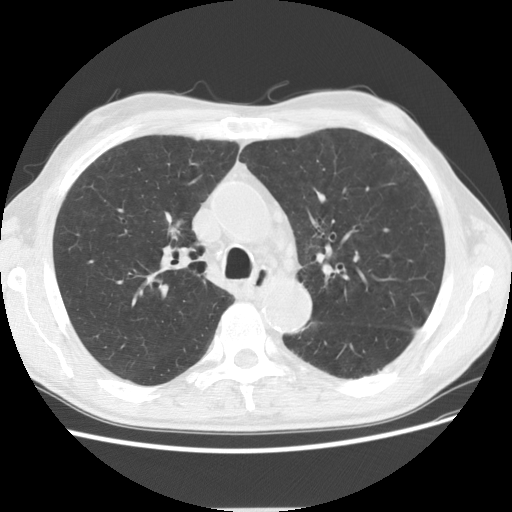
Chest CT (low-dose screening protocol), one axial image. Baseline annual screen. Lung window (W 1500 / L -600 HU). 2.5 mm slice thickness. Standard (soft-tissue) reconstruction kernel (STANDARD). 120 kVp. 512 × 512 image matrix. Male participant, aged 73 years at enrolment. Current smoker at enrolment.
• Expert reader's lesion annotation, bounding box [x1, y1, x2, y2] px = [139, 191, 208, 261].
• Reader record for this screening exam (exam-level; its link to the box is not recorded): non-calcified nodule or mass ≥4 mm, right upper lobe, 16 × 9 mm, spiculated (stellate) margins, soft tissue attenuation.
• Later outcome: lung cancer diagnosed 734 days after this screen (after the third annual screen) — squamous cell carcinoma, NOS, right upper lobe, poorly differentiated (G3), stage IIIB (AJCC 6th edition), 56 mm at pathology.